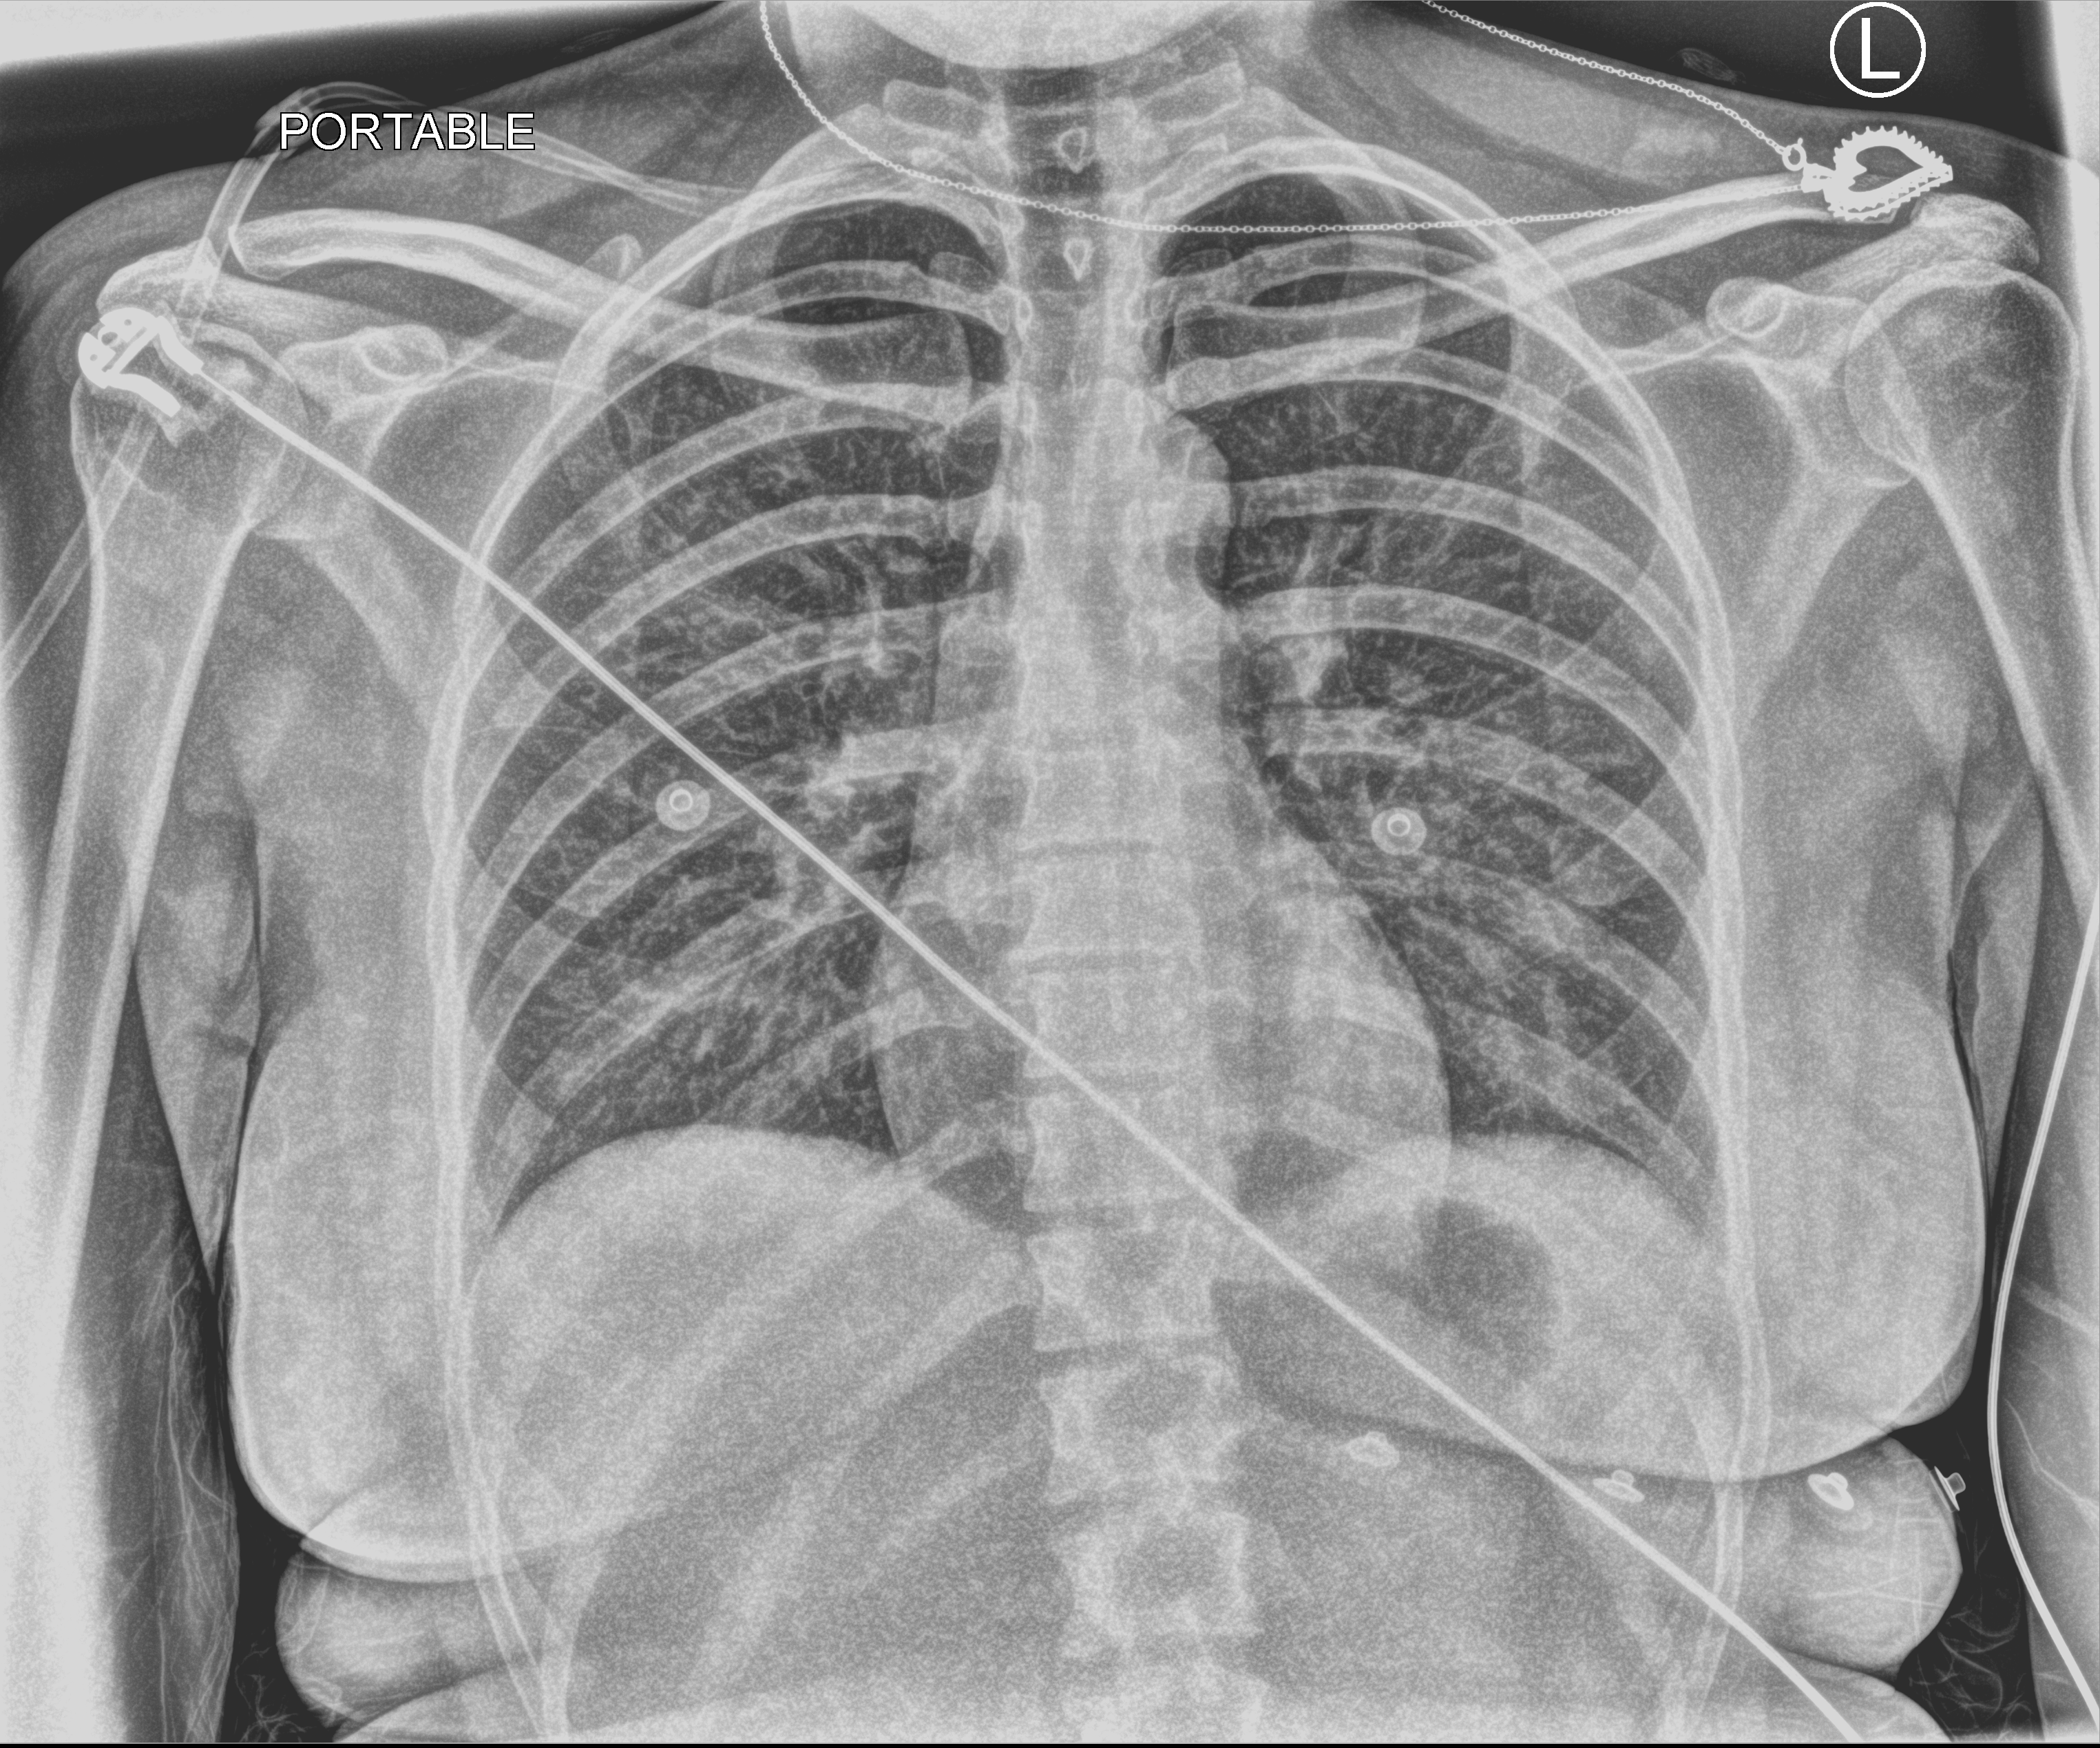
Bedside chest radiograph (computed radiography); anteroposterior (AP) projection. Patient hospitalised with COVID-19; female, aged 18–59 years.
From the hospital-stay record, not from the radiograph (when in the stay this image was taken is not recorded): admitted to intensive care during this hospital stay: no; mechanically ventilated during this hospital stay: no; length of hospital stay: 7 days.